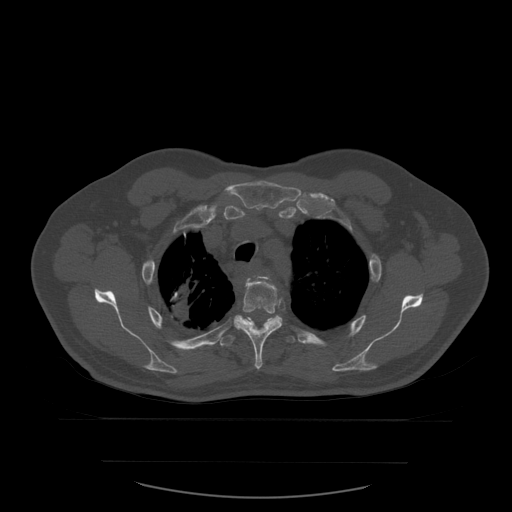
CT including the spine, one axial slice. Slice 440 of 590 in the series (ordered by position). Bone window (W 1800 / L 400 HU). 512 × 512 image matrix, field of view 479 × 479 mm. Patient age 71 years. Case-level facts recorded for this patient, not image findings: primary cancer: lung.
Annotated regions visible in this slice (semi-automatic segmentation, software-assisted and operator-edited):
- T3 vertebra: bounding box <250,275,270,281> (left, top, right, bottom; pixels)
- T4 vertebra: <234,276,283,370>
- T5 vertebra: <220,319,296,347>